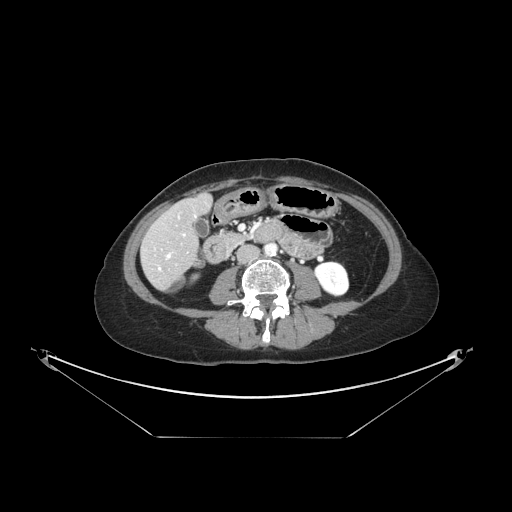
Contrast-enhanced abdominal CT, one axial slice; position 41 of 148 along the scan axis; reconstruction kernel STANDARD; 120 kVp; intravenous contrast given; soft-tissue window (W 400 / L 40 HU); 512 × 512 image matrix, field of view 500 × 500 mm. Female patient, age 73 years. From the clinical record (not read from this slice): diagnosis: colorectal cancer liver metastases, imaged before liver resection; multiple liver metastases: no; largest metastasis: 1 cm; disease in both lobes: no.
Outlined on this slice (outlined manually by an expert reader):
- hepatic veins: bounding box [x1, y1, x2, y2] px = [158, 234, 185, 270]
- liver: [143, 197, 212, 289]
- planned liver remnant (the part of the liver to remain after resection): [161, 197, 211, 241]